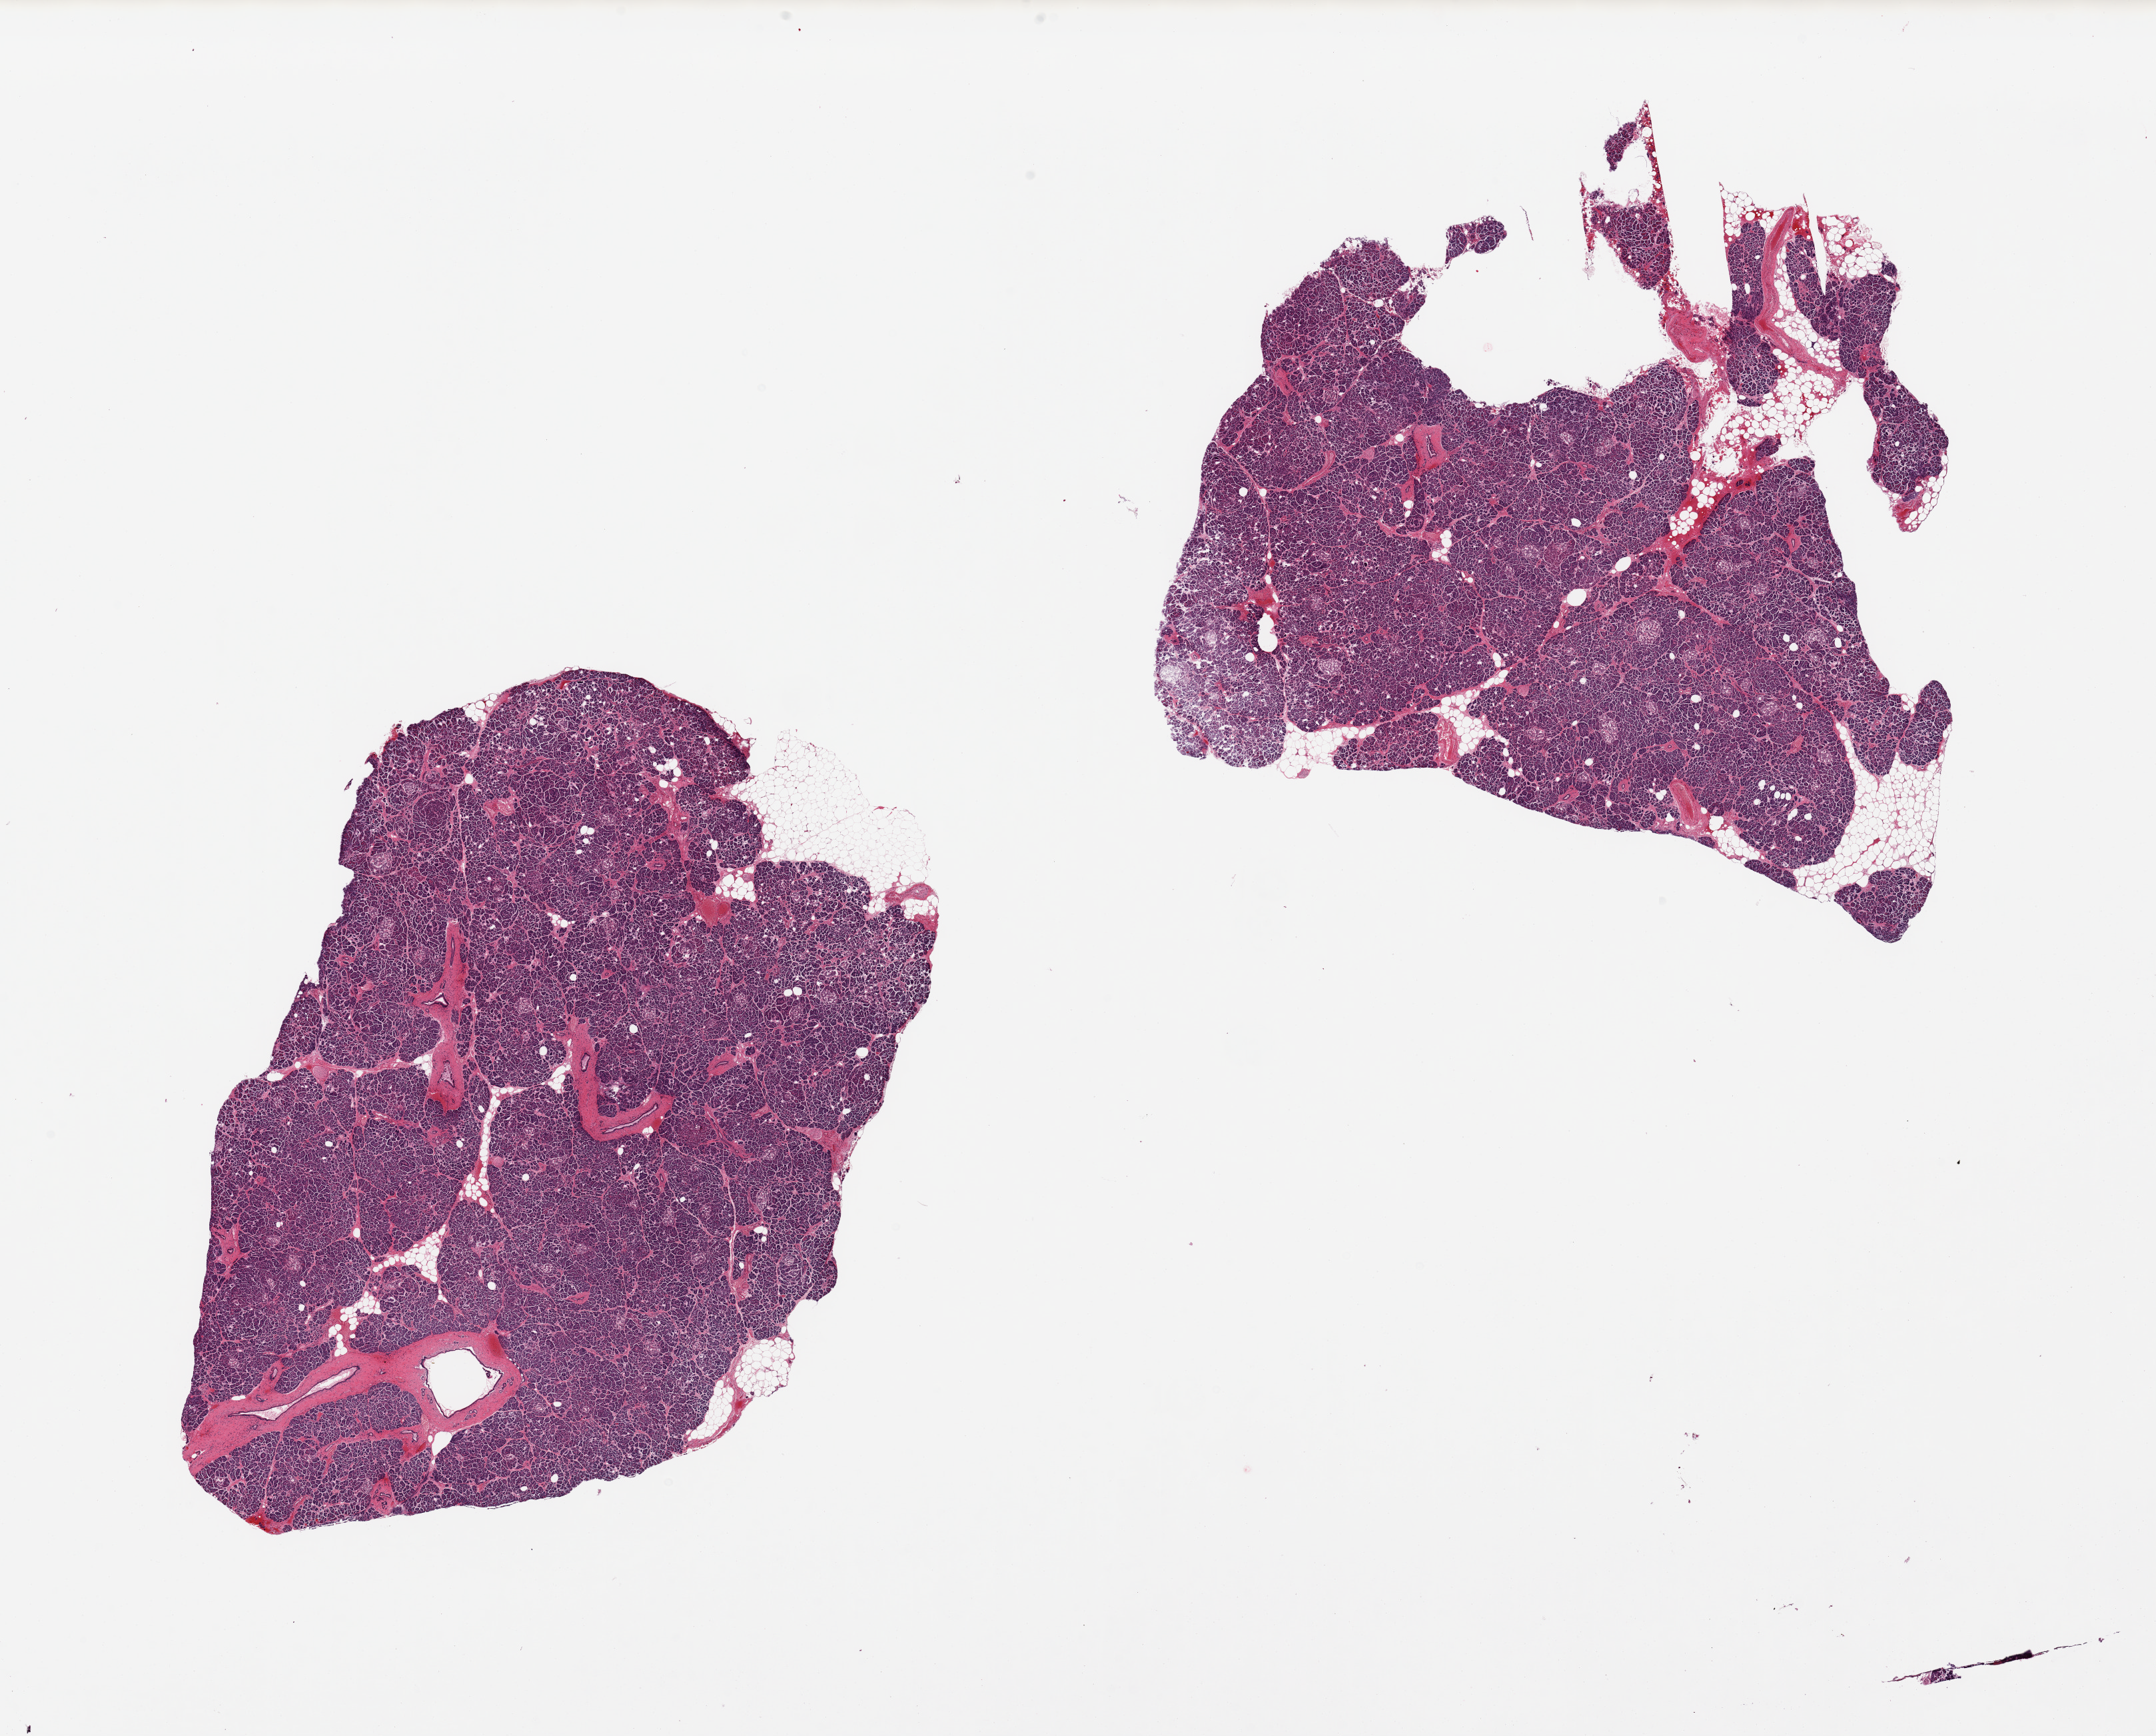
Whole-slide image, H&E stain — whole scanned area (about 25.6 x 20.6 mm) shown as a low-resolution overview. PAXgene-fixed paraffin-embedded (PFPE) section. Target tissue: pancreas. Donor tissue sample. Donor sex: female.
Reviewer comment on this tissue sample: 2 pieces, moderate-marked saponification/autolysis; islets still well visualized.